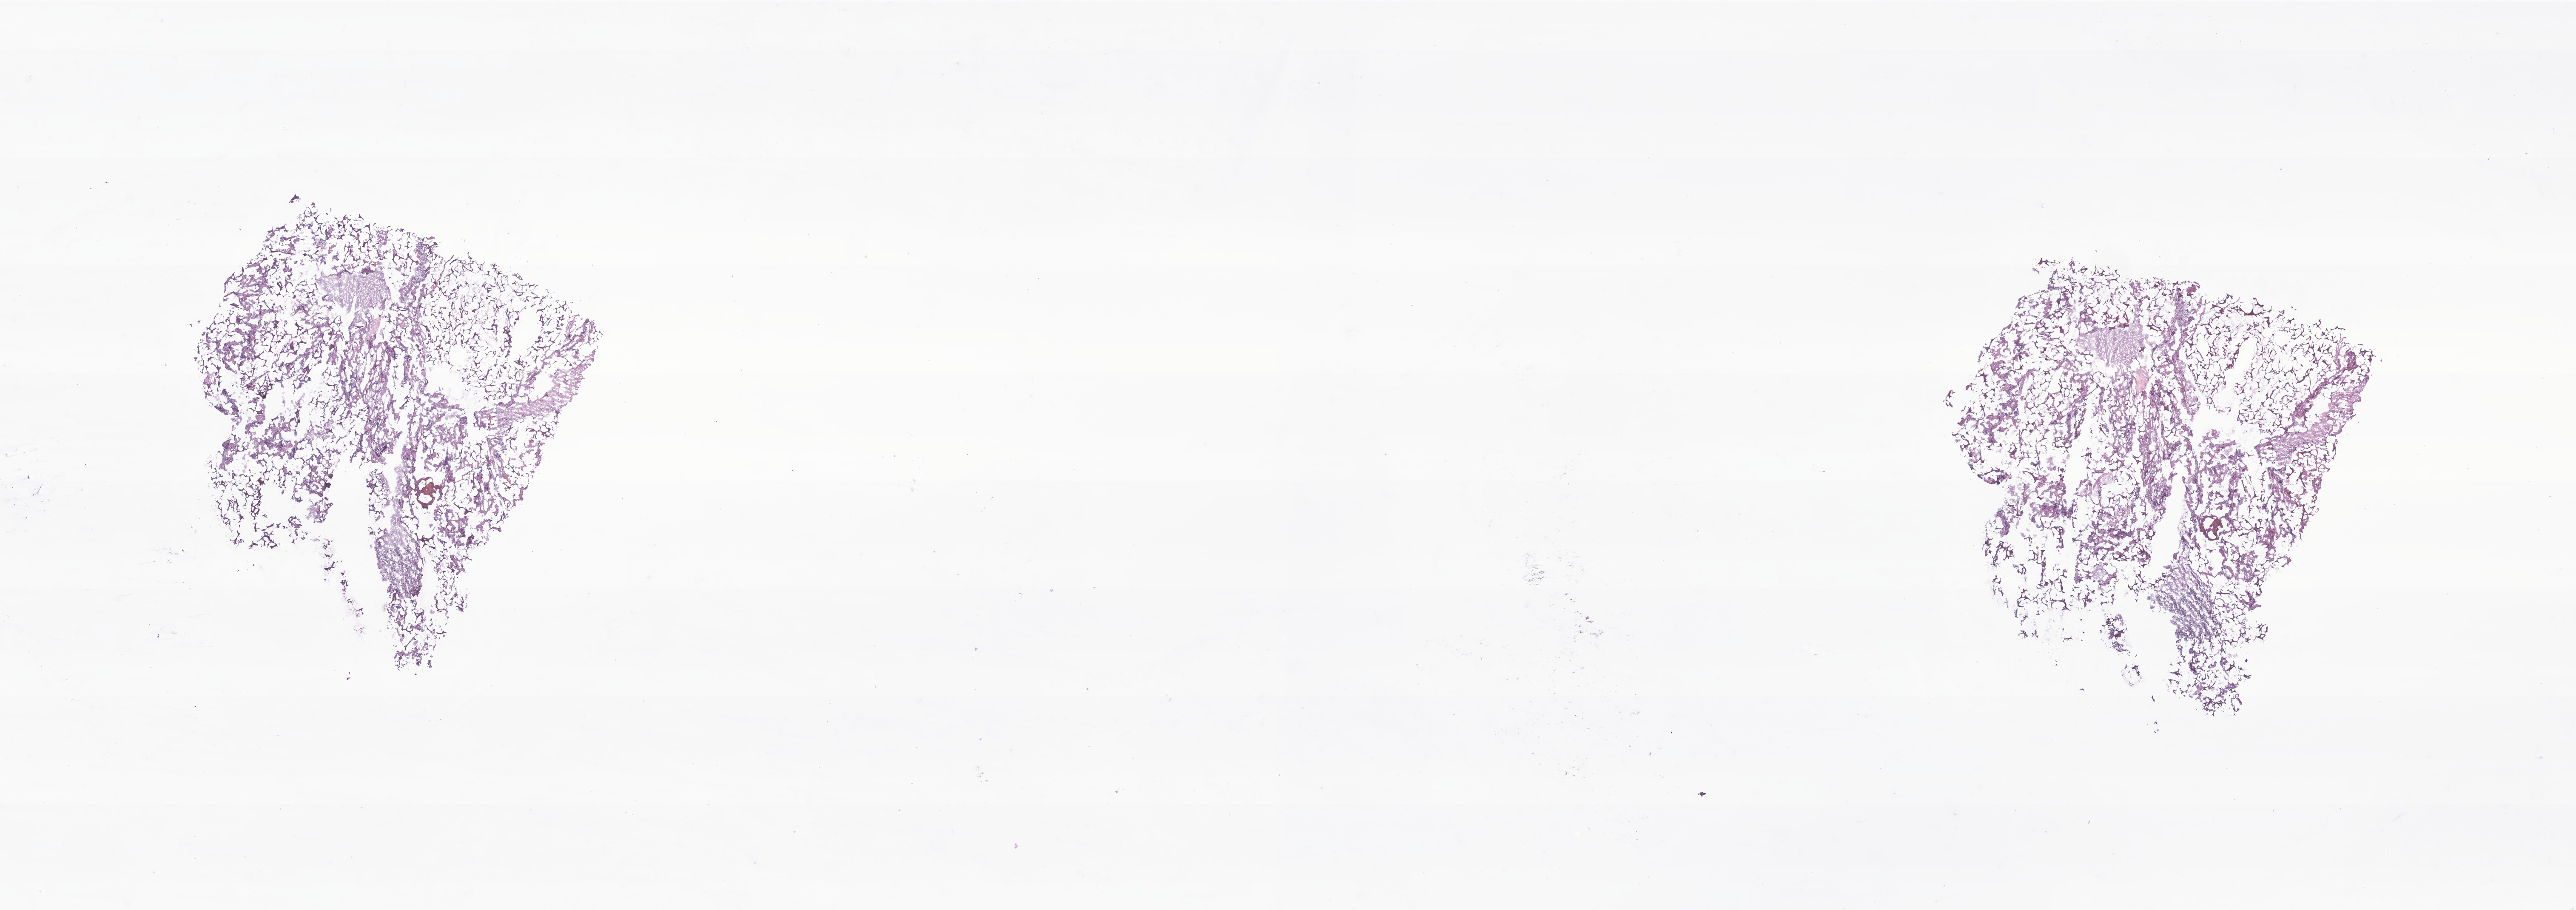
Haematoxylin and eosin whole-slide image of tumor tissue from the brain — whole scanned area (about 25.5 x 9.0 mm) shown as a low-resolution overview; cryosection (OCT / tissue freezing medium). Patient female; age 198 months (16 years 6 months).
Diagnosis: Medulloblastoma, NOS.